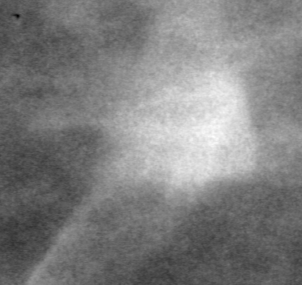
Region of interest cut from a scanned film mammogram (one marked finding), left breast, MLO view, BI-RADS breast density category 2 (scale 1–4).
Mass, shape irregular, margins ill defined; BI-RADS assessment category 4; pathology (as recorded): malignant.